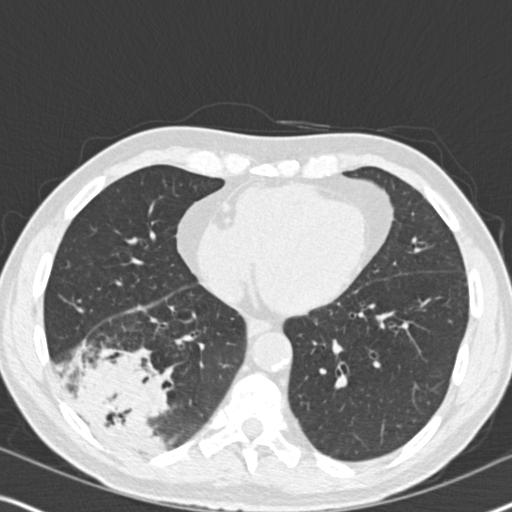
Chest CT (low-dose screening protocol), one axial image; second annual screen; lung window (W 1500 / L -600 HU); 2 mm slice thickness; standard (soft-tissue) reconstruction kernel (B30f). Male participant, aged 61 years at enrolment.
Lesion marked by an expert reader, bounding box [x1, y1, x2, y2] px = [47, 322, 188, 463]. The exam's reader record, not a measurement of the box and not confirmed to be the same lesion: non-calcified nodule or mass ≥4 mm, right lower lobe, 90 × 80 mm, soft tissue attenuation, pre-existing on the prior screen: yes; interval growth: yes. Official screen result: positive, other. Later outcome: lung cancer diagnosed 20 days after this screen — bronchiolo-alveolar adenocarcinoma, NOS, right lower lobe, moderately differentiated (G2), stage IIIB (AJCC 6th edition), 90 mm at pathology.